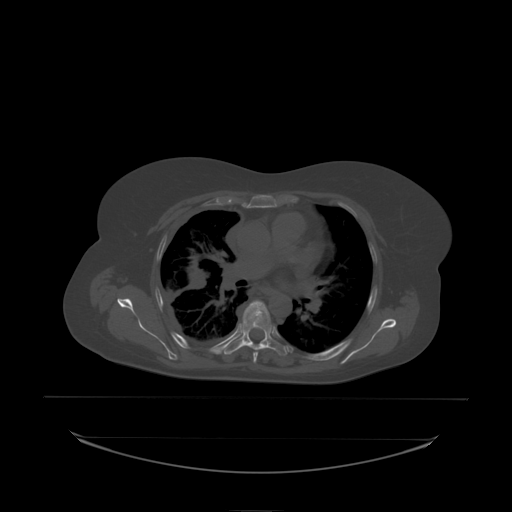
CT including the spine, one axial slice; slice 153 of 242 in the series (ordered by position); bone window (W 1800 / L 400 HU); 2.5 mm slice thickness; 512 × 512 image matrix, field of view 500 × 500 mm. Patient: female, 53 years. Case-level facts recorded for this patient, not image findings: primary cancer: lung.
Outlined on this slice (semi-automatic segmentation, software-assisted and operator-edited):
- T5 vertebra: bounding box [x1, y1, x2, y2] px = [248, 305, 251, 309]
- T6 vertebra: [243, 301, 272, 338]